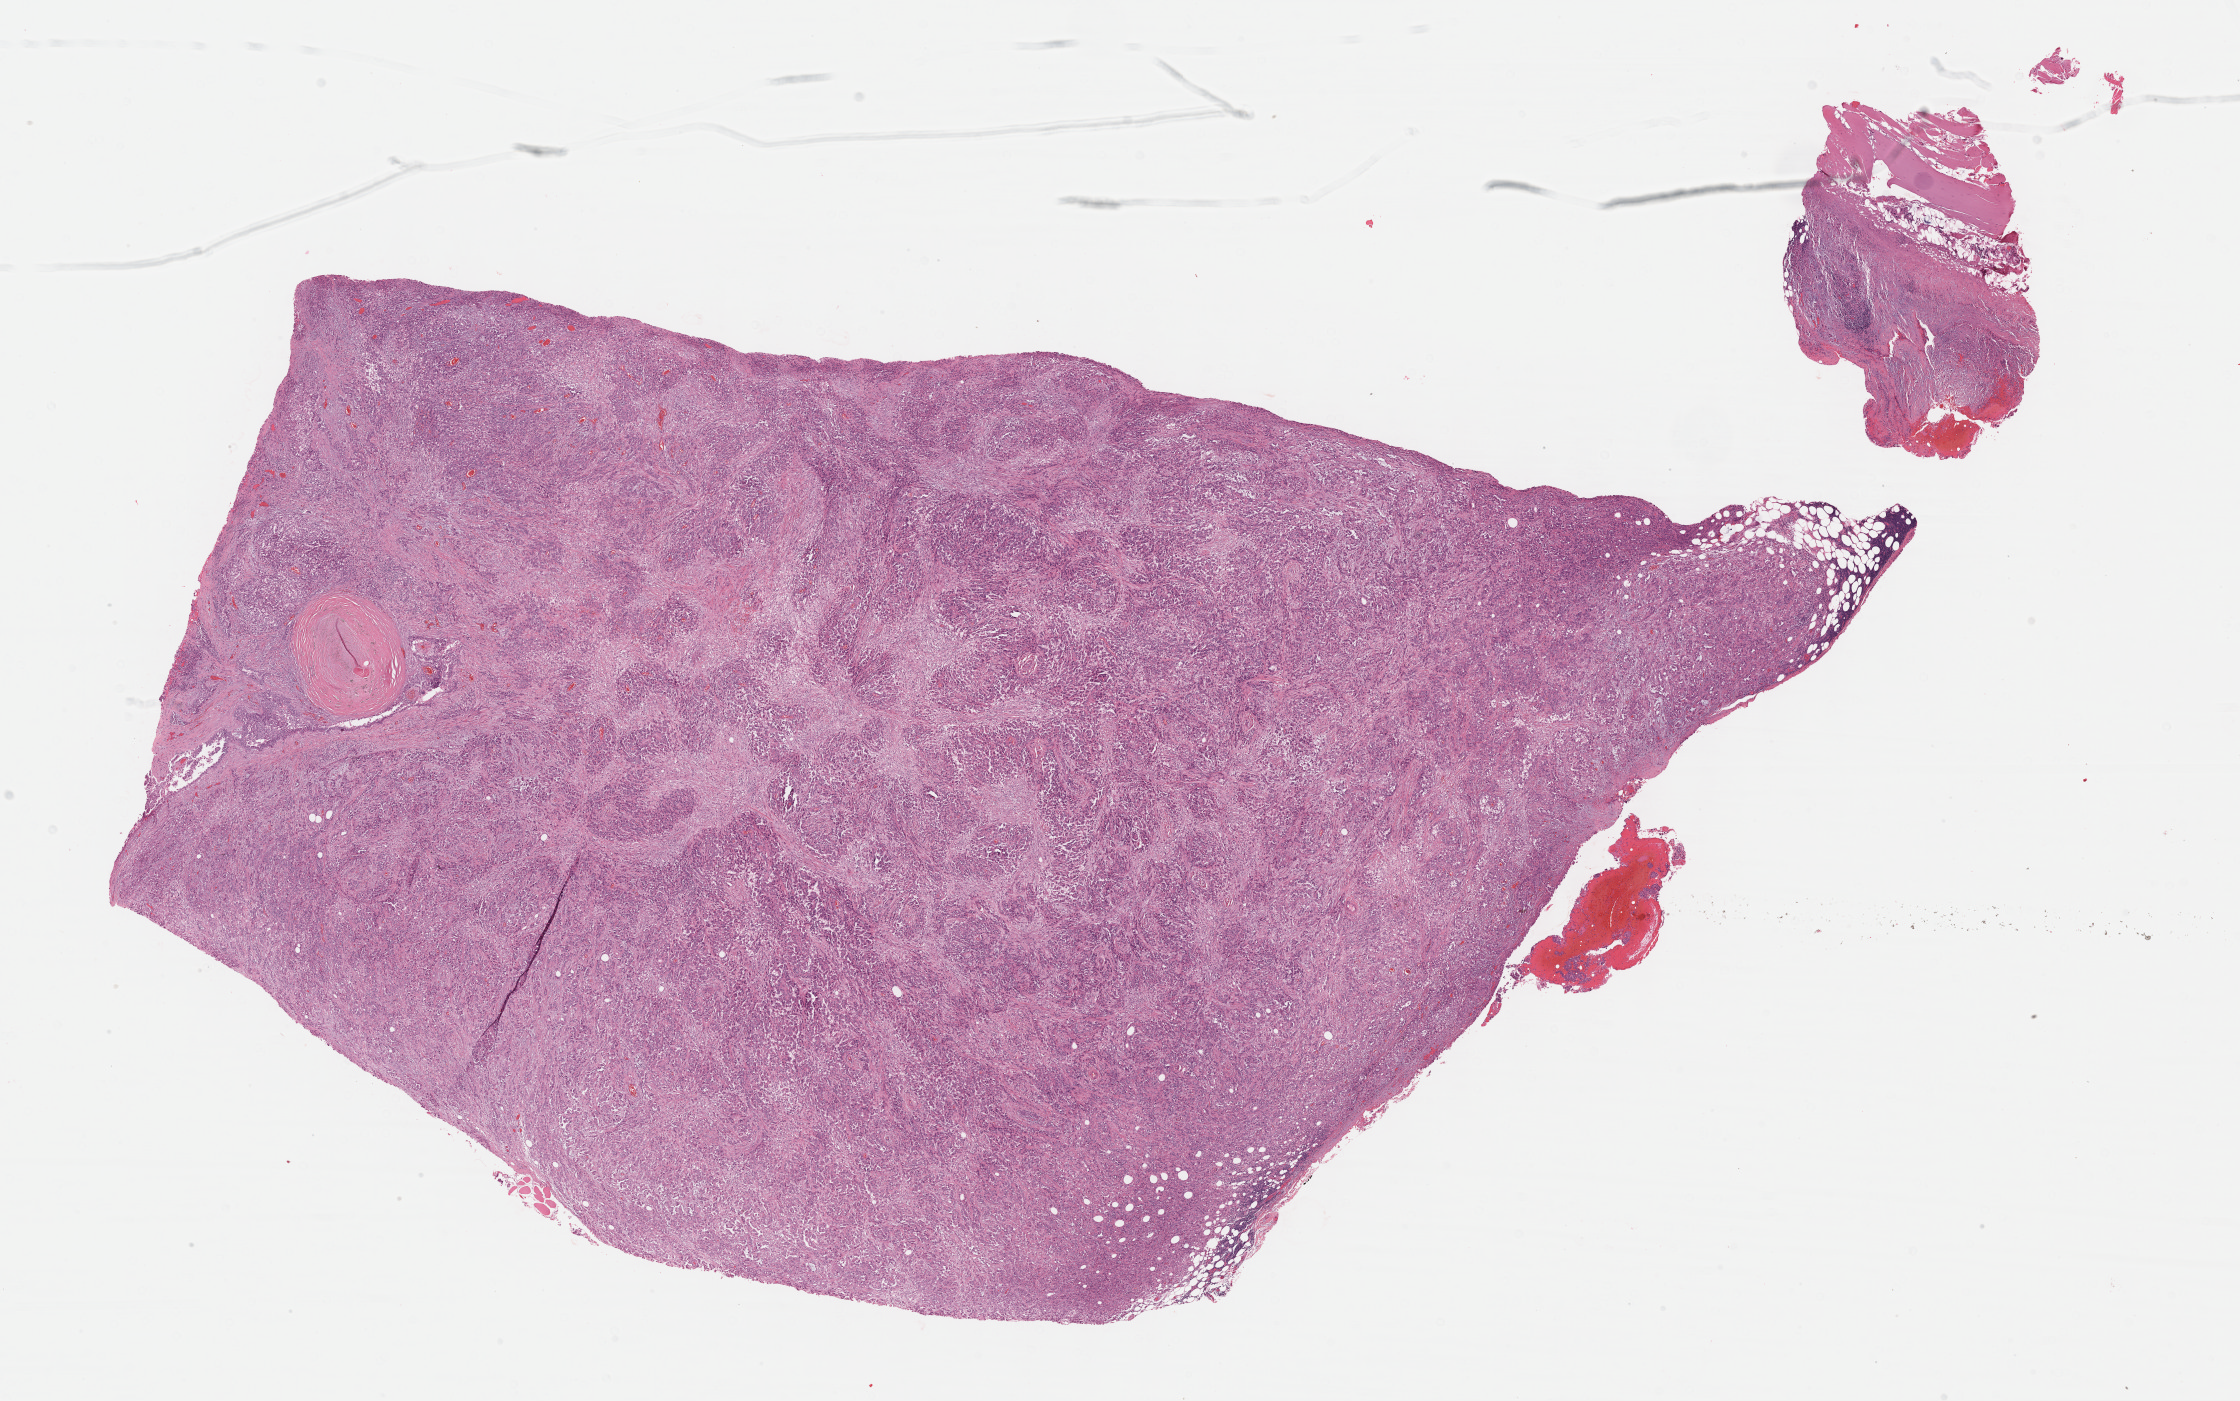
Whole-slide histology image, H&E-stained — shown as a low-resolution overview of the whole scanned area (about 18.1 x 11.3 mm, acquisition: 40x scan); formalin-fixed paraffin-embedded (FFPE) diagnostic section; sample: primary tumour, mesothelium. Male patient; age at initial diagnosis 69 years.
Diagnosis: Epithelioid mesothelioma, malignant.